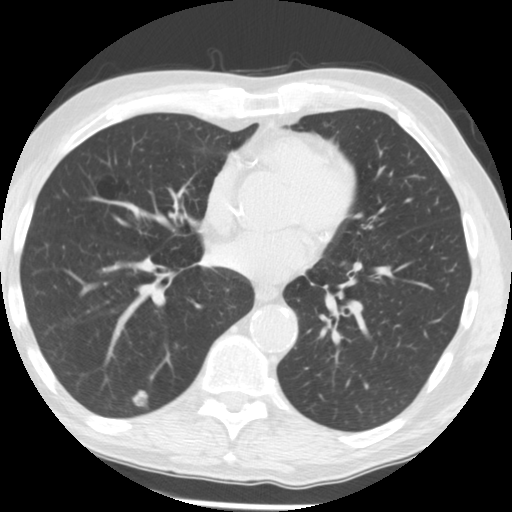
Chest CT (low-dose screening protocol), one axial image; second annual screen; lung window (W 1500 / L -600 HU); 512 × 512 image matrix. Male participant, aged 62 years at enrolment. Current smoker at enrolment.
• Lesion marked by an expert reader, box from (x=127, y=384) to (x=164, y=415) px.
• The screening reader recorded 2 non-calcified nodules or masses ≥4 mm on this exam (right lower lobe, right lower lobe); which of them this box marks is not recorded.